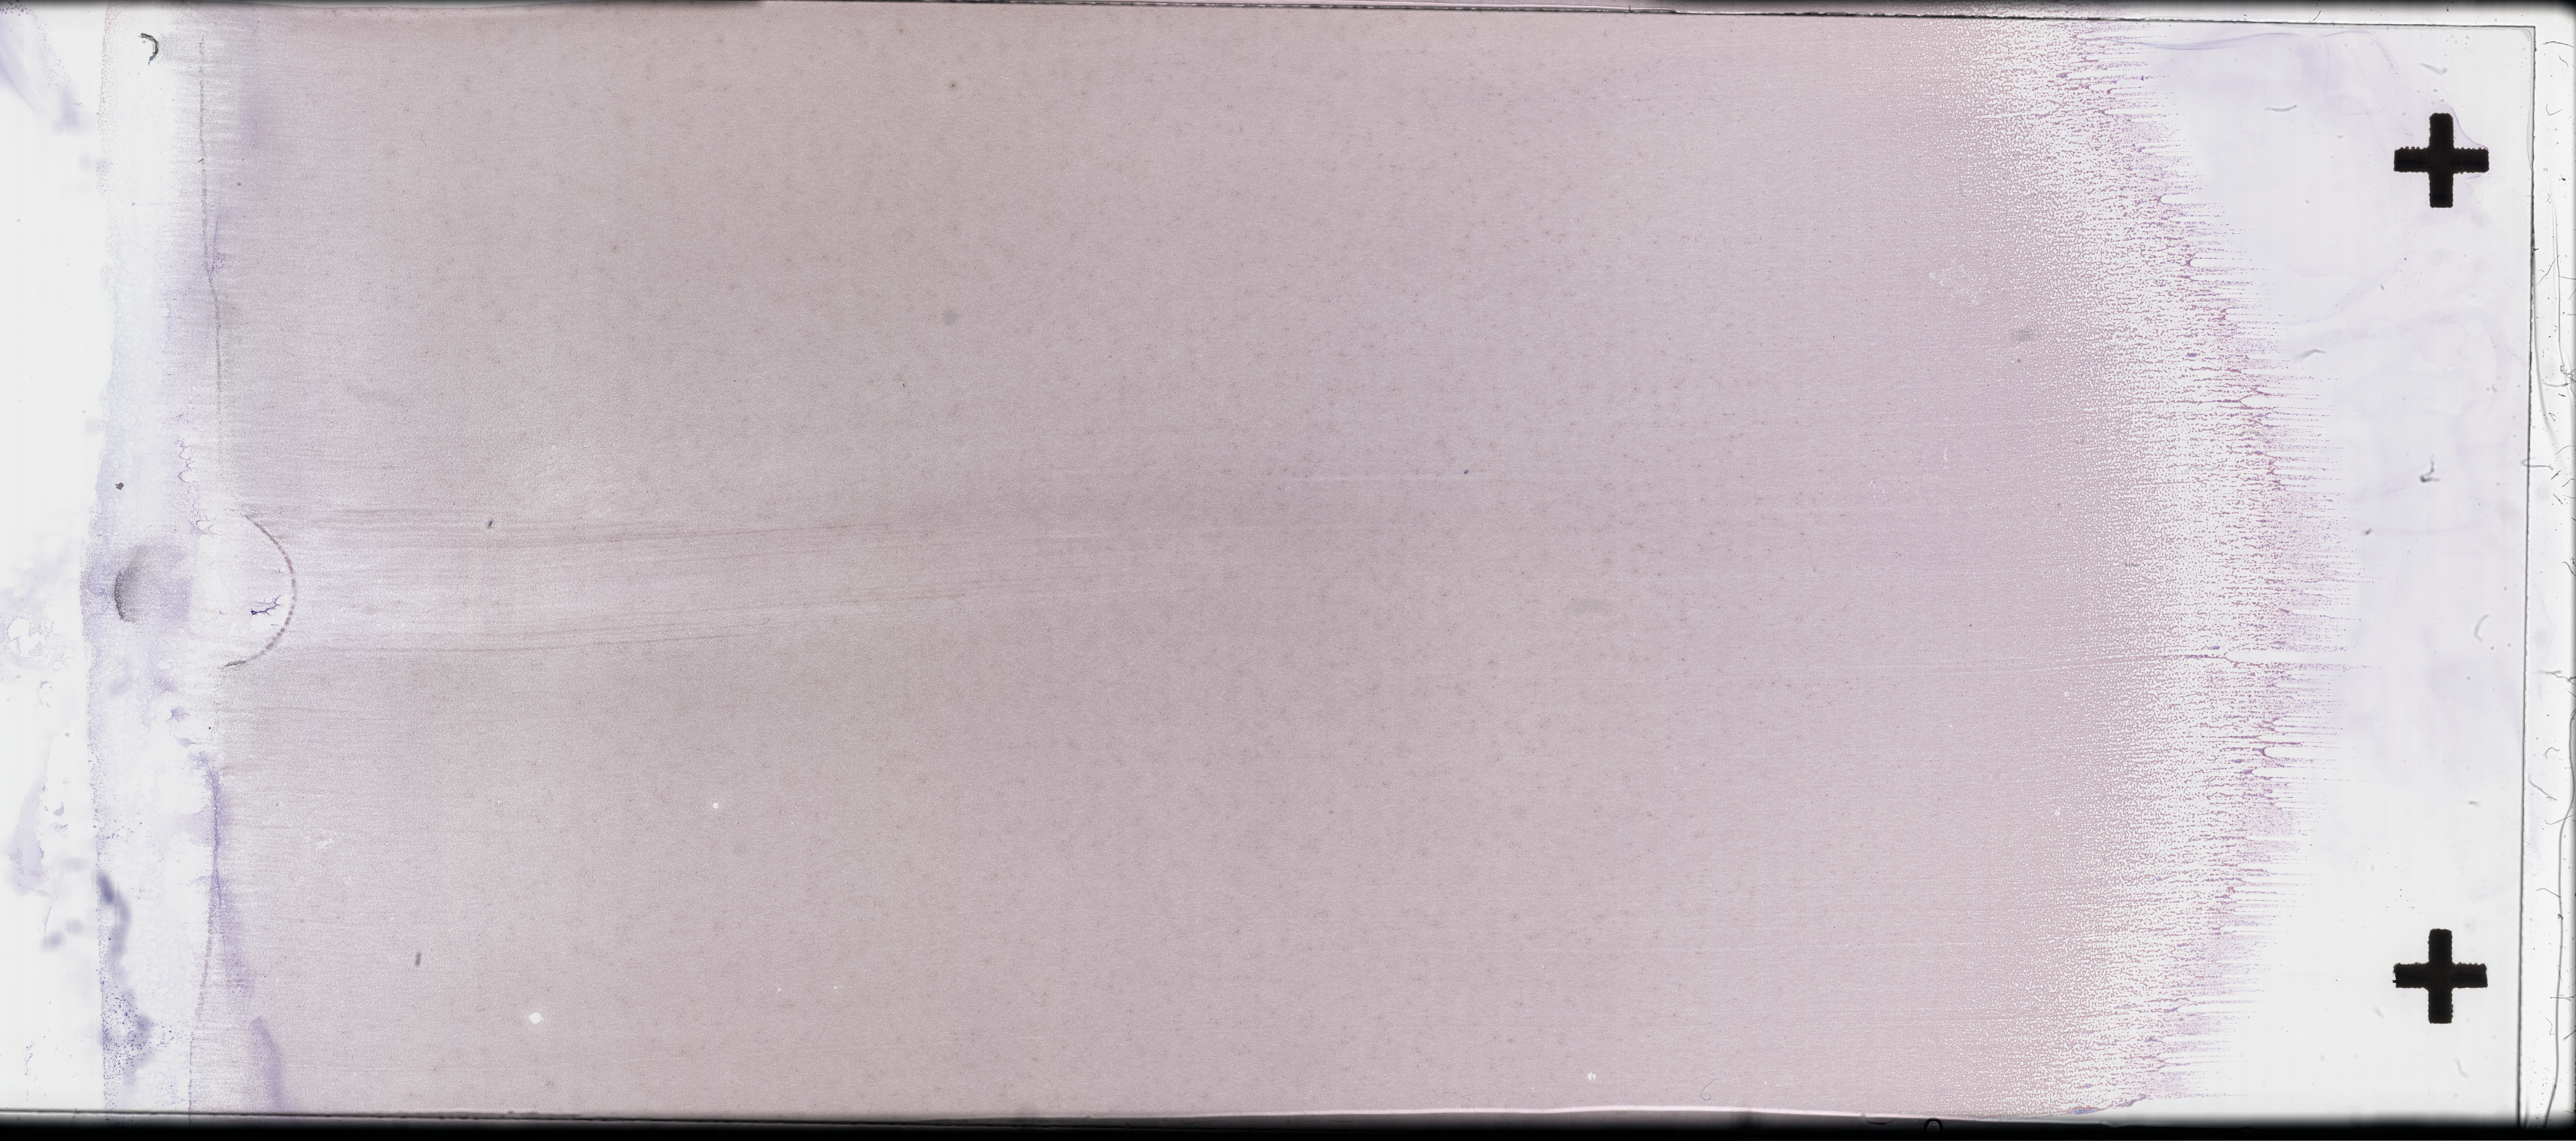
Whole-slide image of a whole blood smear, Wright–Giemsa stain — shown as a low-resolution overview of the whole scanned area (about 55.3 x 24.5 mm). Patient: male.
* from a patient with: Plasma Cell Myeloma